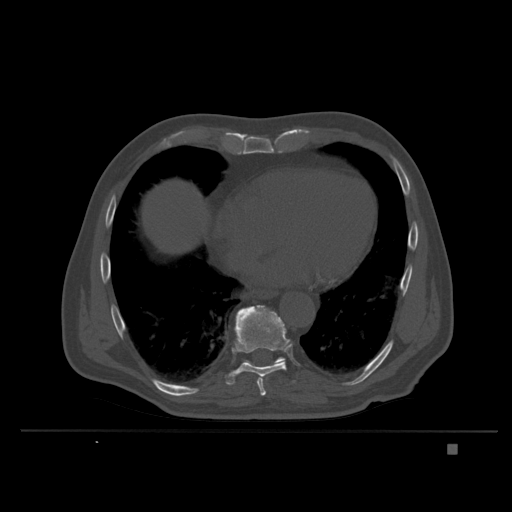
CT including the spine, one axial slice; slice 210 of 435 in the series (ordered by position); bone window (W 1800 / L 400 HU); 1.5 mm slice thickness; 512 × 512 image matrix. Male patient, age 73 years. Case-level facts recorded for this patient, not image findings: primary cancer: skin.
Outlined on this slice (semi-automatically segmented with operator editing):
- T10 vertebra: bounding box <244,357,285,367> (left, top, right, bottom; pixels)
- T9 vertebra: <226,305,296,396>